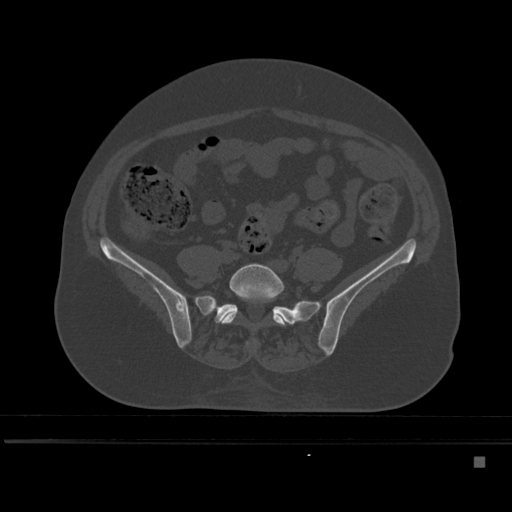
CT including the spine, one axial slice. Slice 102 of 495 in the series (ordered by position). Bone window (W 1800 / L 400 HU). 1.5 mm slice thickness. 512 × 512 image matrix, field of view 404 × 404 mm. Patient: female, 33 years. From the clinical record (not read from this slice): primary cancer: breast.
Annotated regions visible in this slice (semi-automatic segmentation, software-assisted and operator-edited):
- L5 vertebra: bounding box <220,263,289,347> (left, top, right, bottom; pixels)